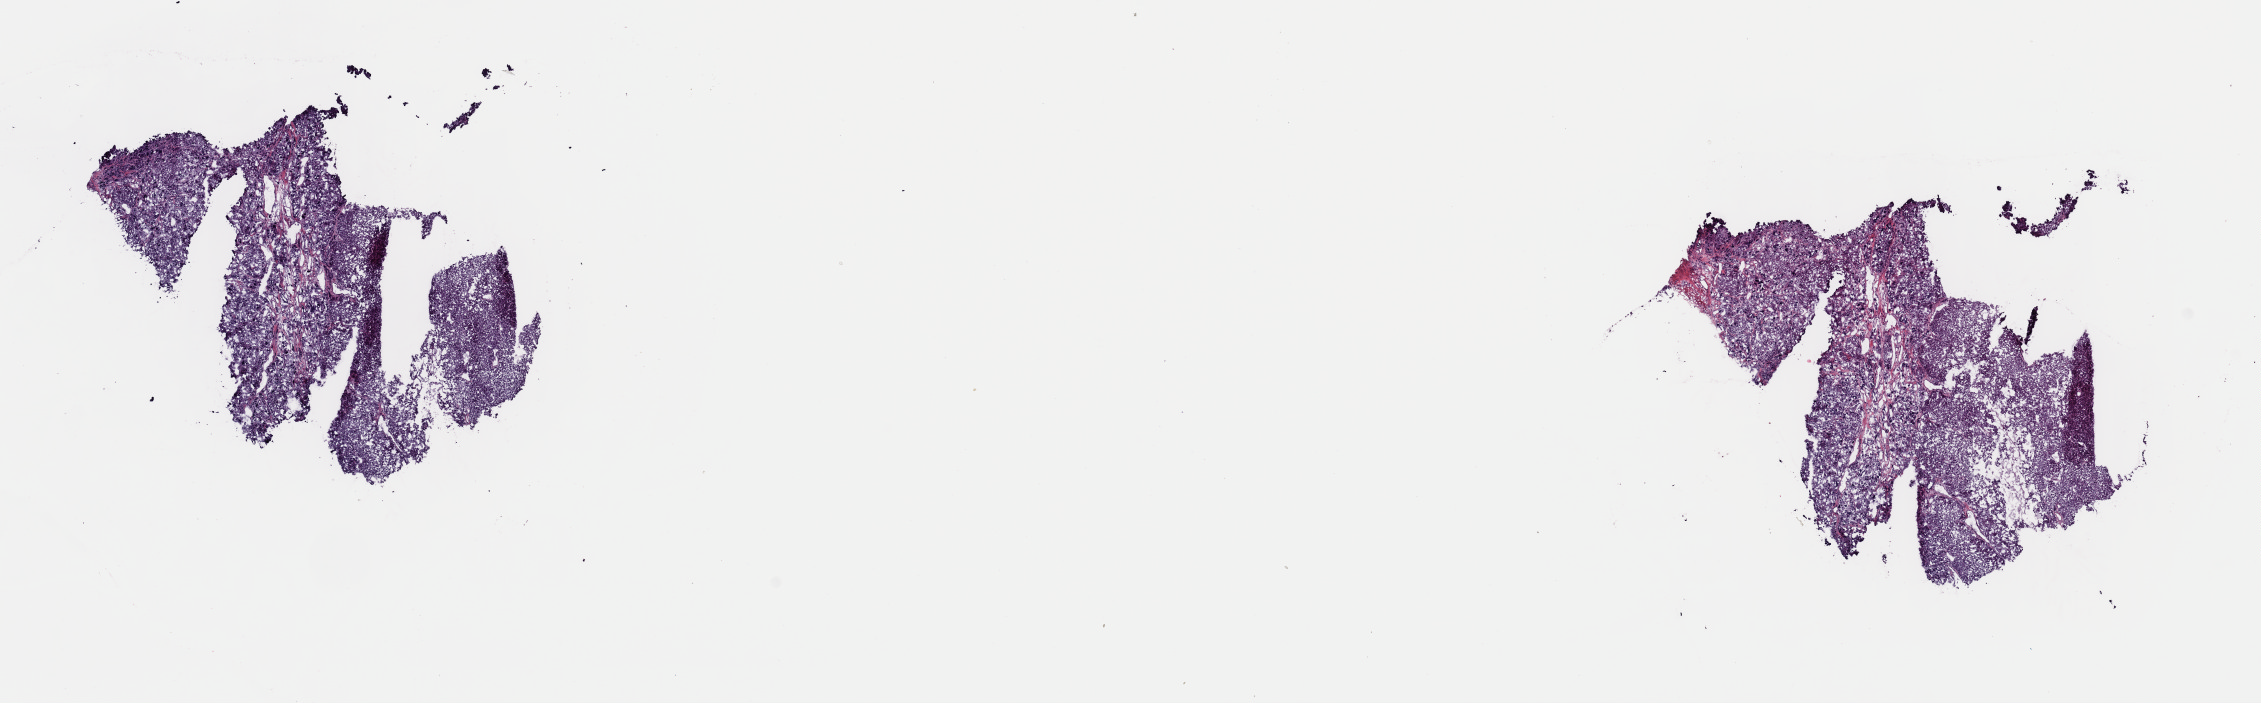
Whole-slide histology image, H&E-stained, low-resolution overview of the scanned area, about 17.9 x 5.6 mm (acquisition: 40x scan); frozen section; sample: primary tumour, adrenal cortex. Female, age 39 years at initial diagnosis. Pathologist review of this section (percent, as recorded): tumour cells 99%, tumour nuclei 99%, normal cells 0%, stromal cells 1%, necrosis 0%. Inflammatory infiltration, as recorded: lymphocyte infiltration 0%, monocyte infiltration 0%, neutrophil infiltration 0%.
- diagnosis: Adrenal cortical carcinoma (cortex of adrenal gland)